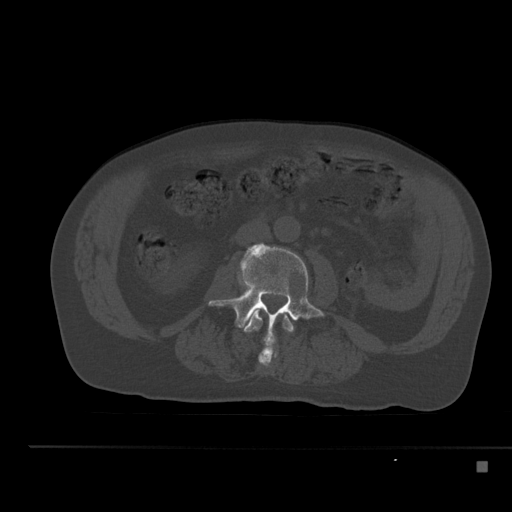
CT including the spine, one axial slice. Slice 168 of 517 in the series (ordered by position). Bone window (W 1800 / L 400 HU). 1.5 mm slice thickness. 512 × 512 image matrix. Male patient, age 70 years. Case-level facts recorded for this patient, not image findings: primary cancer: renal.
Annotated regions visible in this slice (semi-automatically segmented with operator editing):
- L2 vertebra: bounding box [x1, y1, x2, y2] px = [242, 310, 294, 367]
- L3 vertebra: [209, 242, 326, 345]